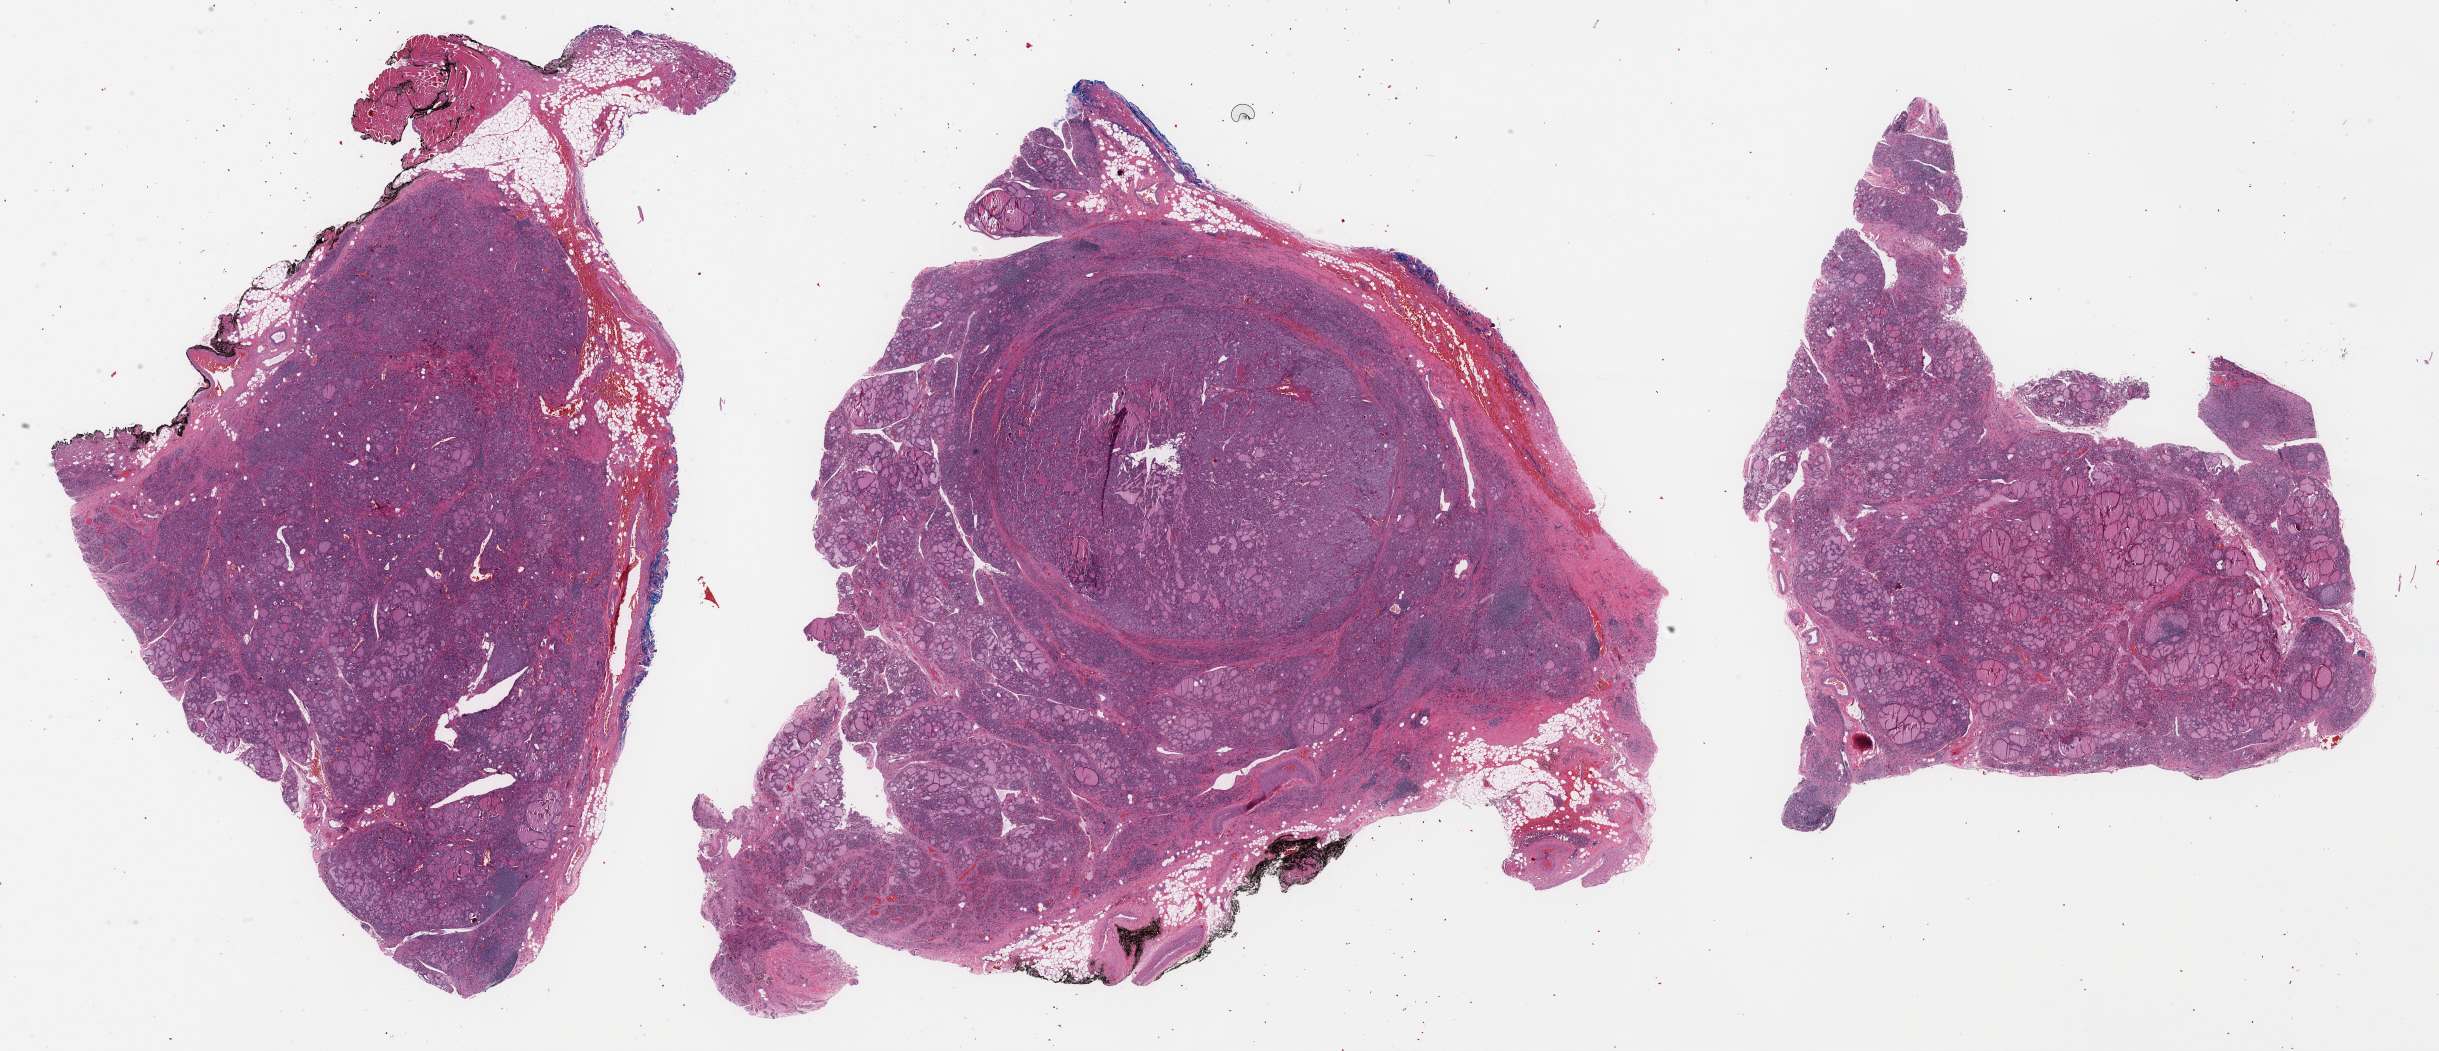
Whole-slide histology image, H&E-stained — a low-resolution overview of the entire scanned area, about 38.5 x 16.6 mm (slide scanned at 40x). Formalin-fixed paraffin-embedded (FFPE) diagnostic section. Sample: primary tumour, thyroid. Male, age 38 years at initial diagnosis.
Diagnosis: Papillary carcinoma, follicular variant (thyroid gland).